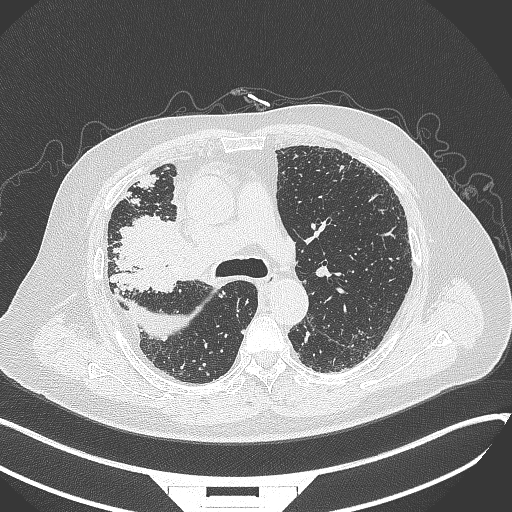
Chest CT, one axial slice; position 225 of 384 along the scan axis; reconstruction kernel B70f; 120 kVp; lung window (W 1500 / L -600 HU); 512 × 512 image matrix, field of view 400 × 400 mm. Male patient, age 69 years. Case-level facts recorded for this patient, not image findings: clinical TNM (as recorded): T4 N3 M1.
Outlined on this slice (rectangle marked by the reading radiologist):
- lung tumour (recorded histology: adenocarcinoma): bounding box (x1, y1, x2, y2) in pixels: (113, 214, 200, 304)